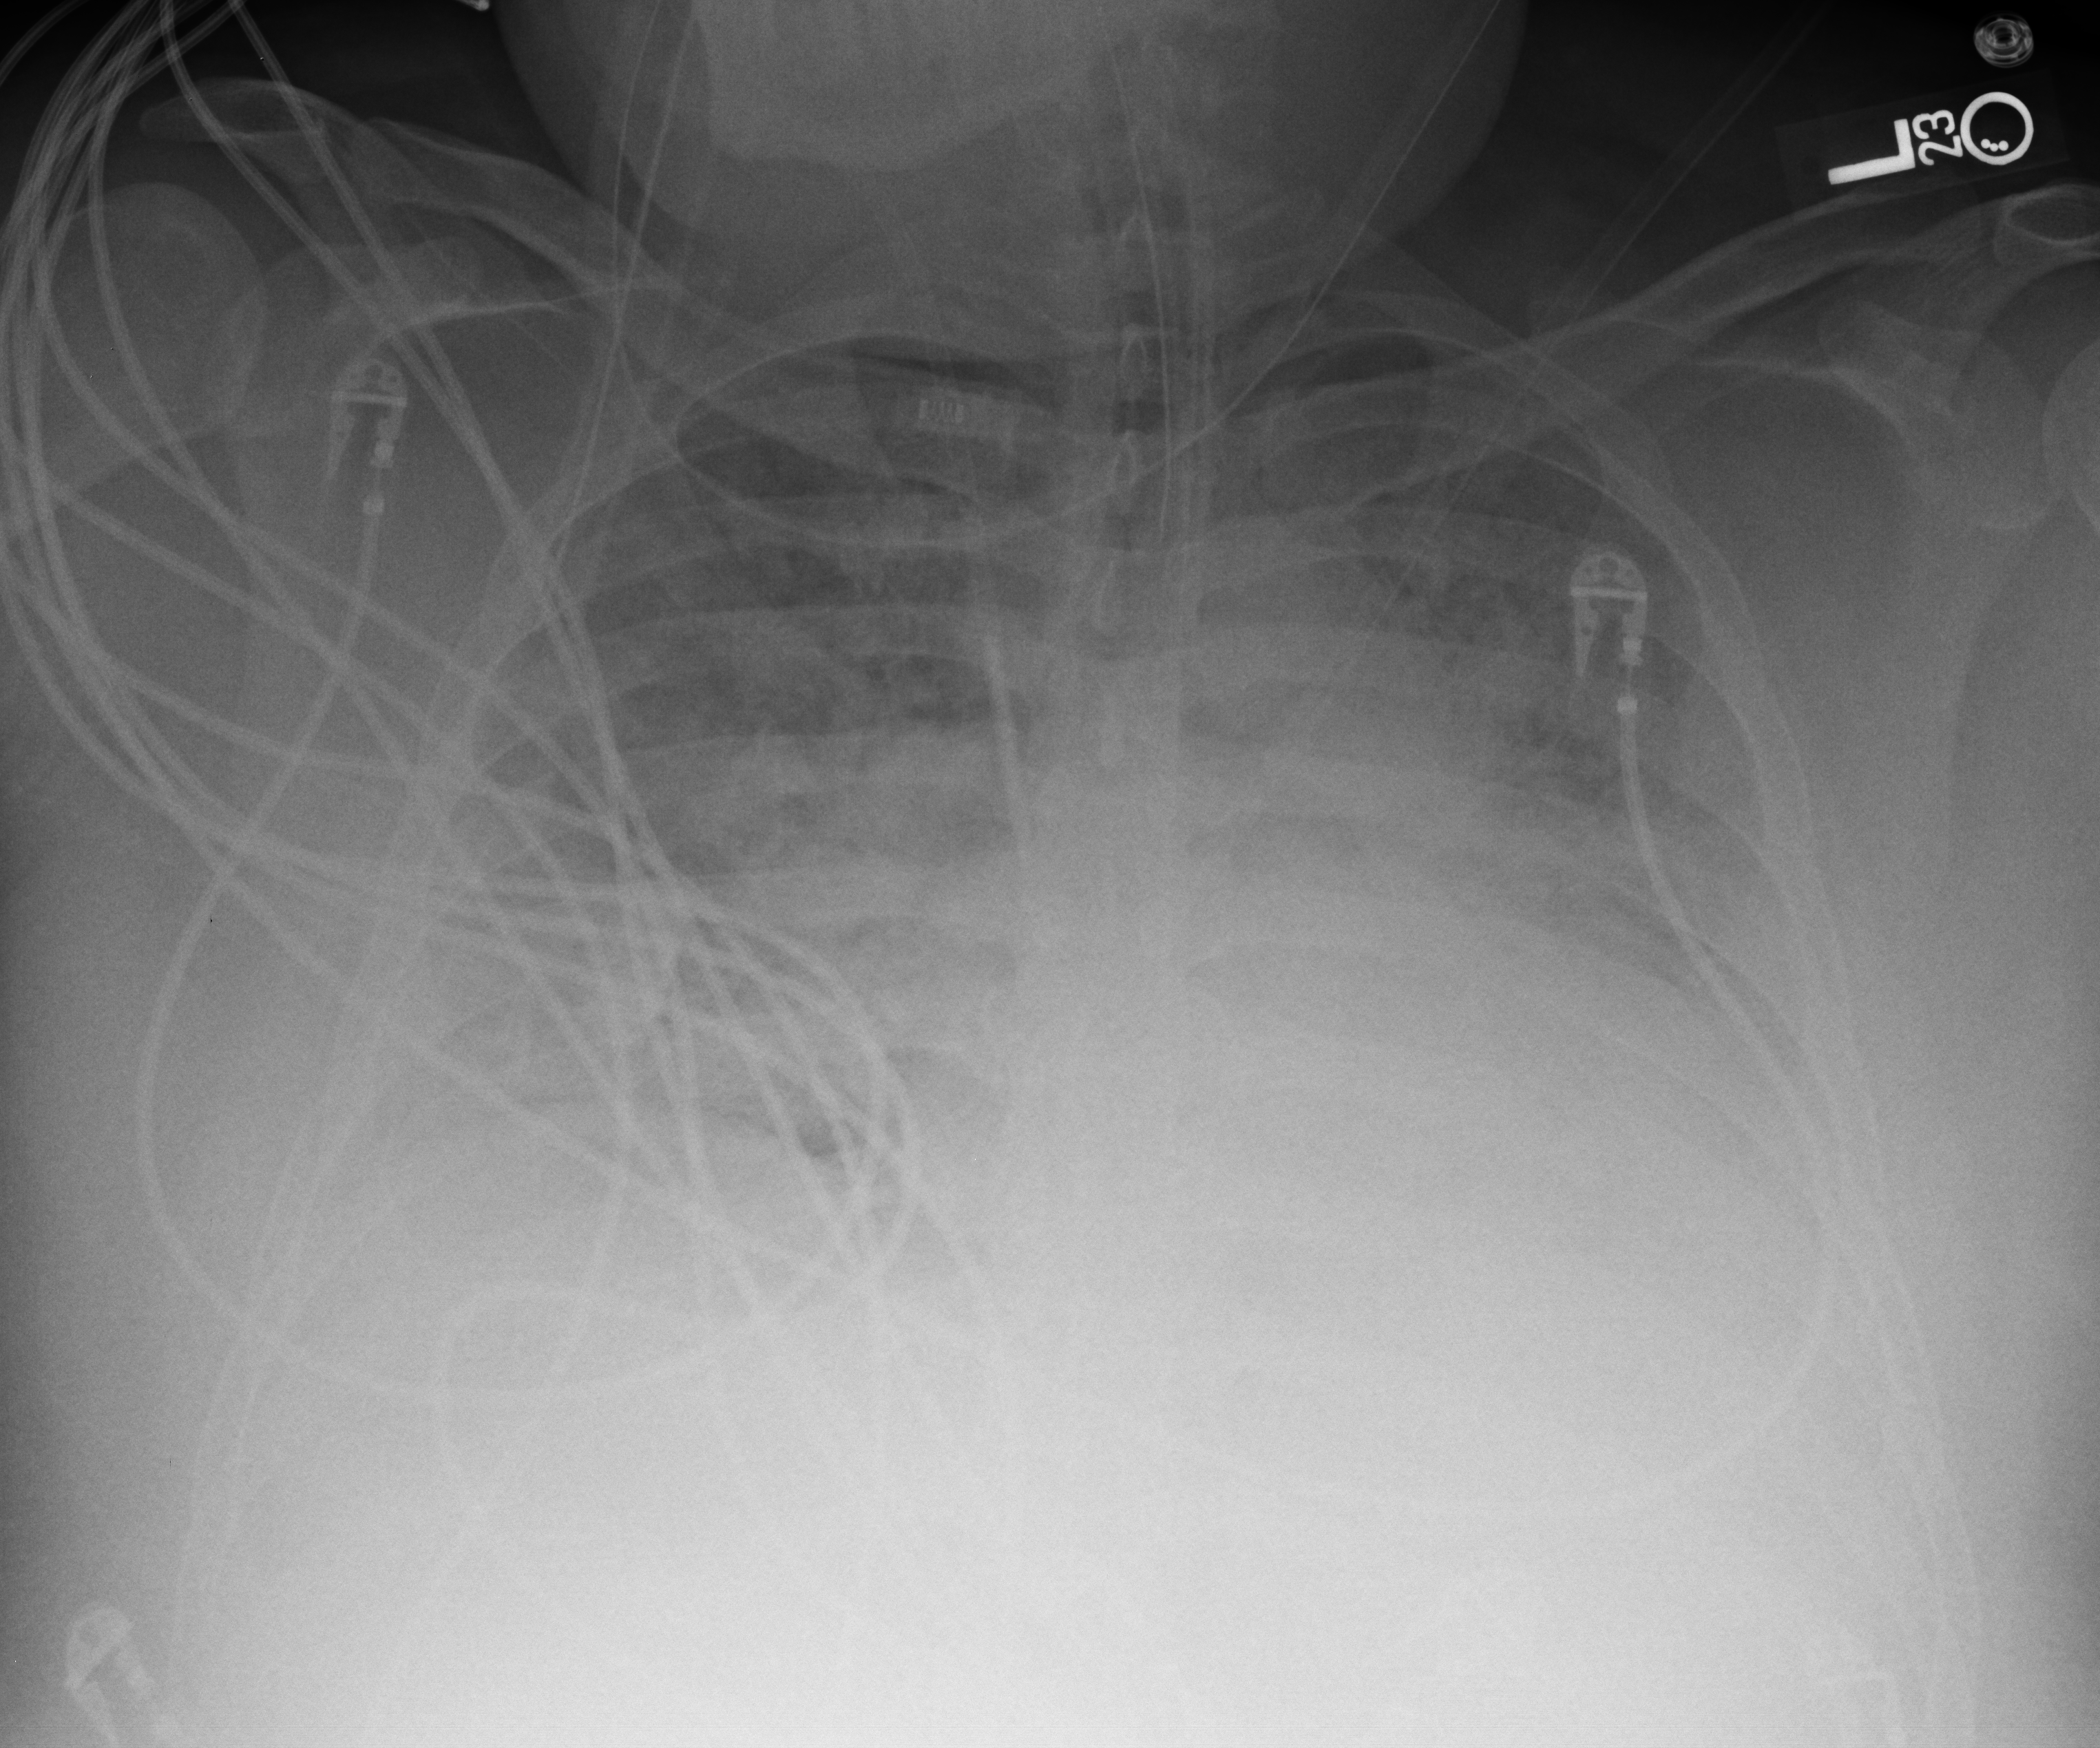
Portable chest radiograph, anteroposterior (AP) projection. Adult patient hospitalised with COVID-19, age 18–59 years.
Admission-level facts for this patient (not findings on this image; timing relative to this image not recorded): mechanically ventilated during this hospital stay: yes; admitted to intensive care during this hospital stay: yes.